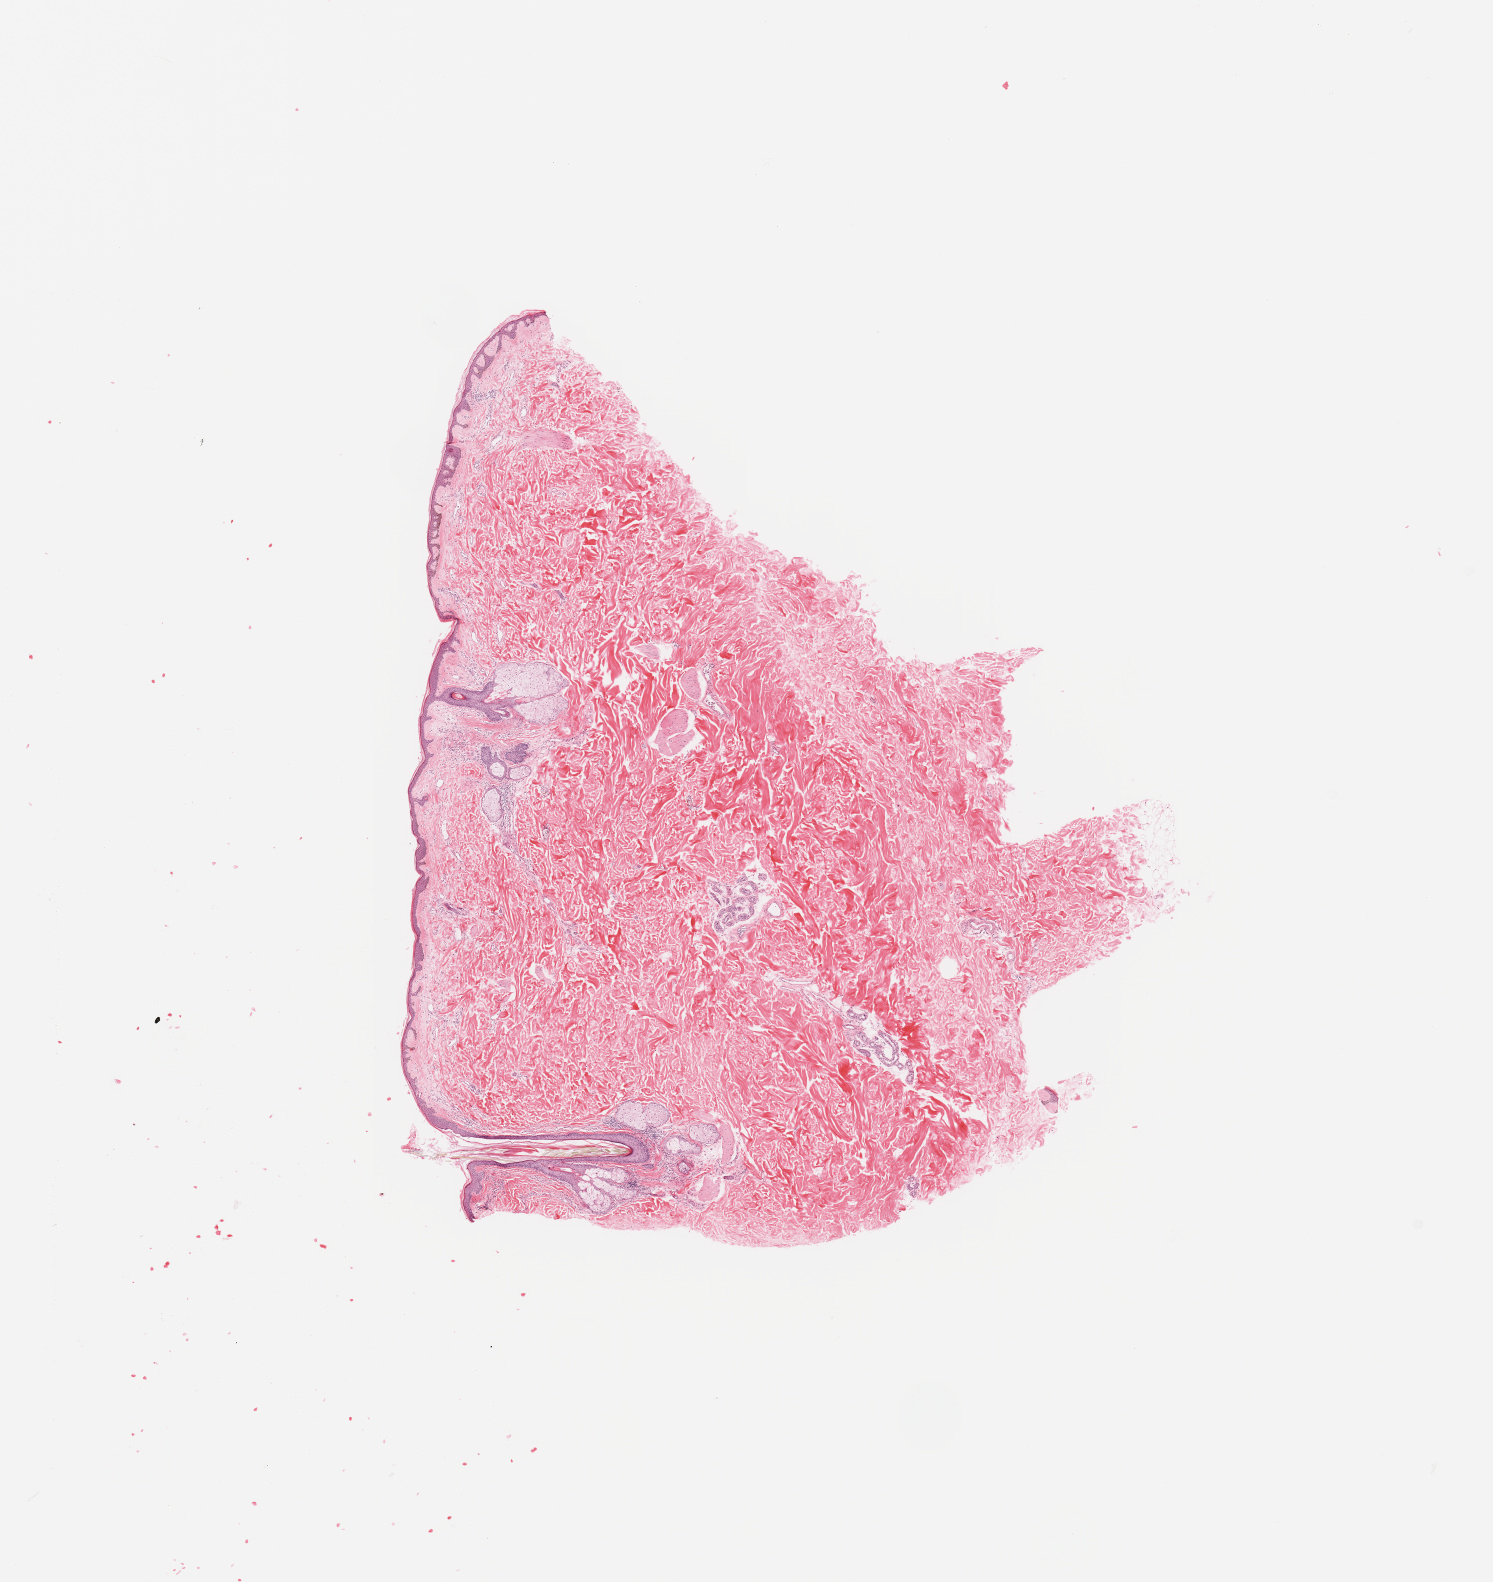
Whole-slide histology image, H&E — whole scanned area (about 11.8 x 12.5 mm) shown as a low-resolution overview, normal (non-tumour) tissue (melanoma cohort); sampled site not recorded. Female, 81 y/o.
This section: normal (non-tumour) tissue from the same patient. Patient diagnosis: Malignant melanoma, NOS.